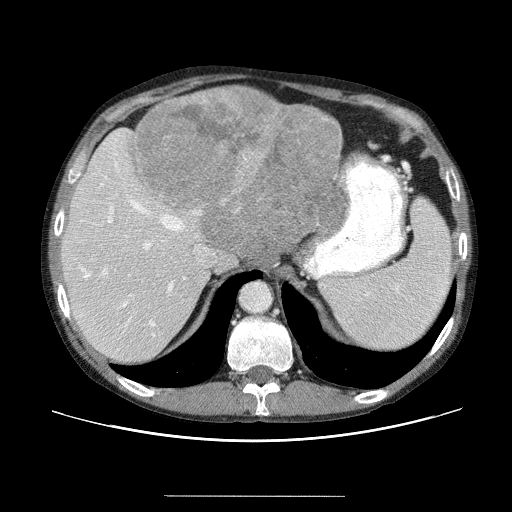
Contrast-enhanced abdominal CT (liver protocol), one axial slice. Slice 42 of 69 in the series (ordered by position). Reconstruction kernel STANDARD. 120 kVp. Soft-tissue window (W 400 / L 40 HU). 2.5 mm slice thickness. 512 × 512 image matrix. Case-level facts recorded for this patient, not image findings: diagnosis: hepatocellular carcinoma (patient treated with transarterial chemoembolisation; whether this scan precedes or follows treatment is not stated here); TNM stage (as recorded): Stage-IVB; Child-Pugh class: B.
Annotated regions visible in this slice (semi-automatic segmentation, software-assisted and operator-edited):
- liver parenchyma outside the tumour (the mass and vessels are separate outlines, so this box may not span the whole liver): box from (x=60, y=96) to (x=343, y=366) px
- mass: (x=130, y=85)–(x=343, y=271)
- liver vessels: (x=94, y=155)–(x=202, y=336)